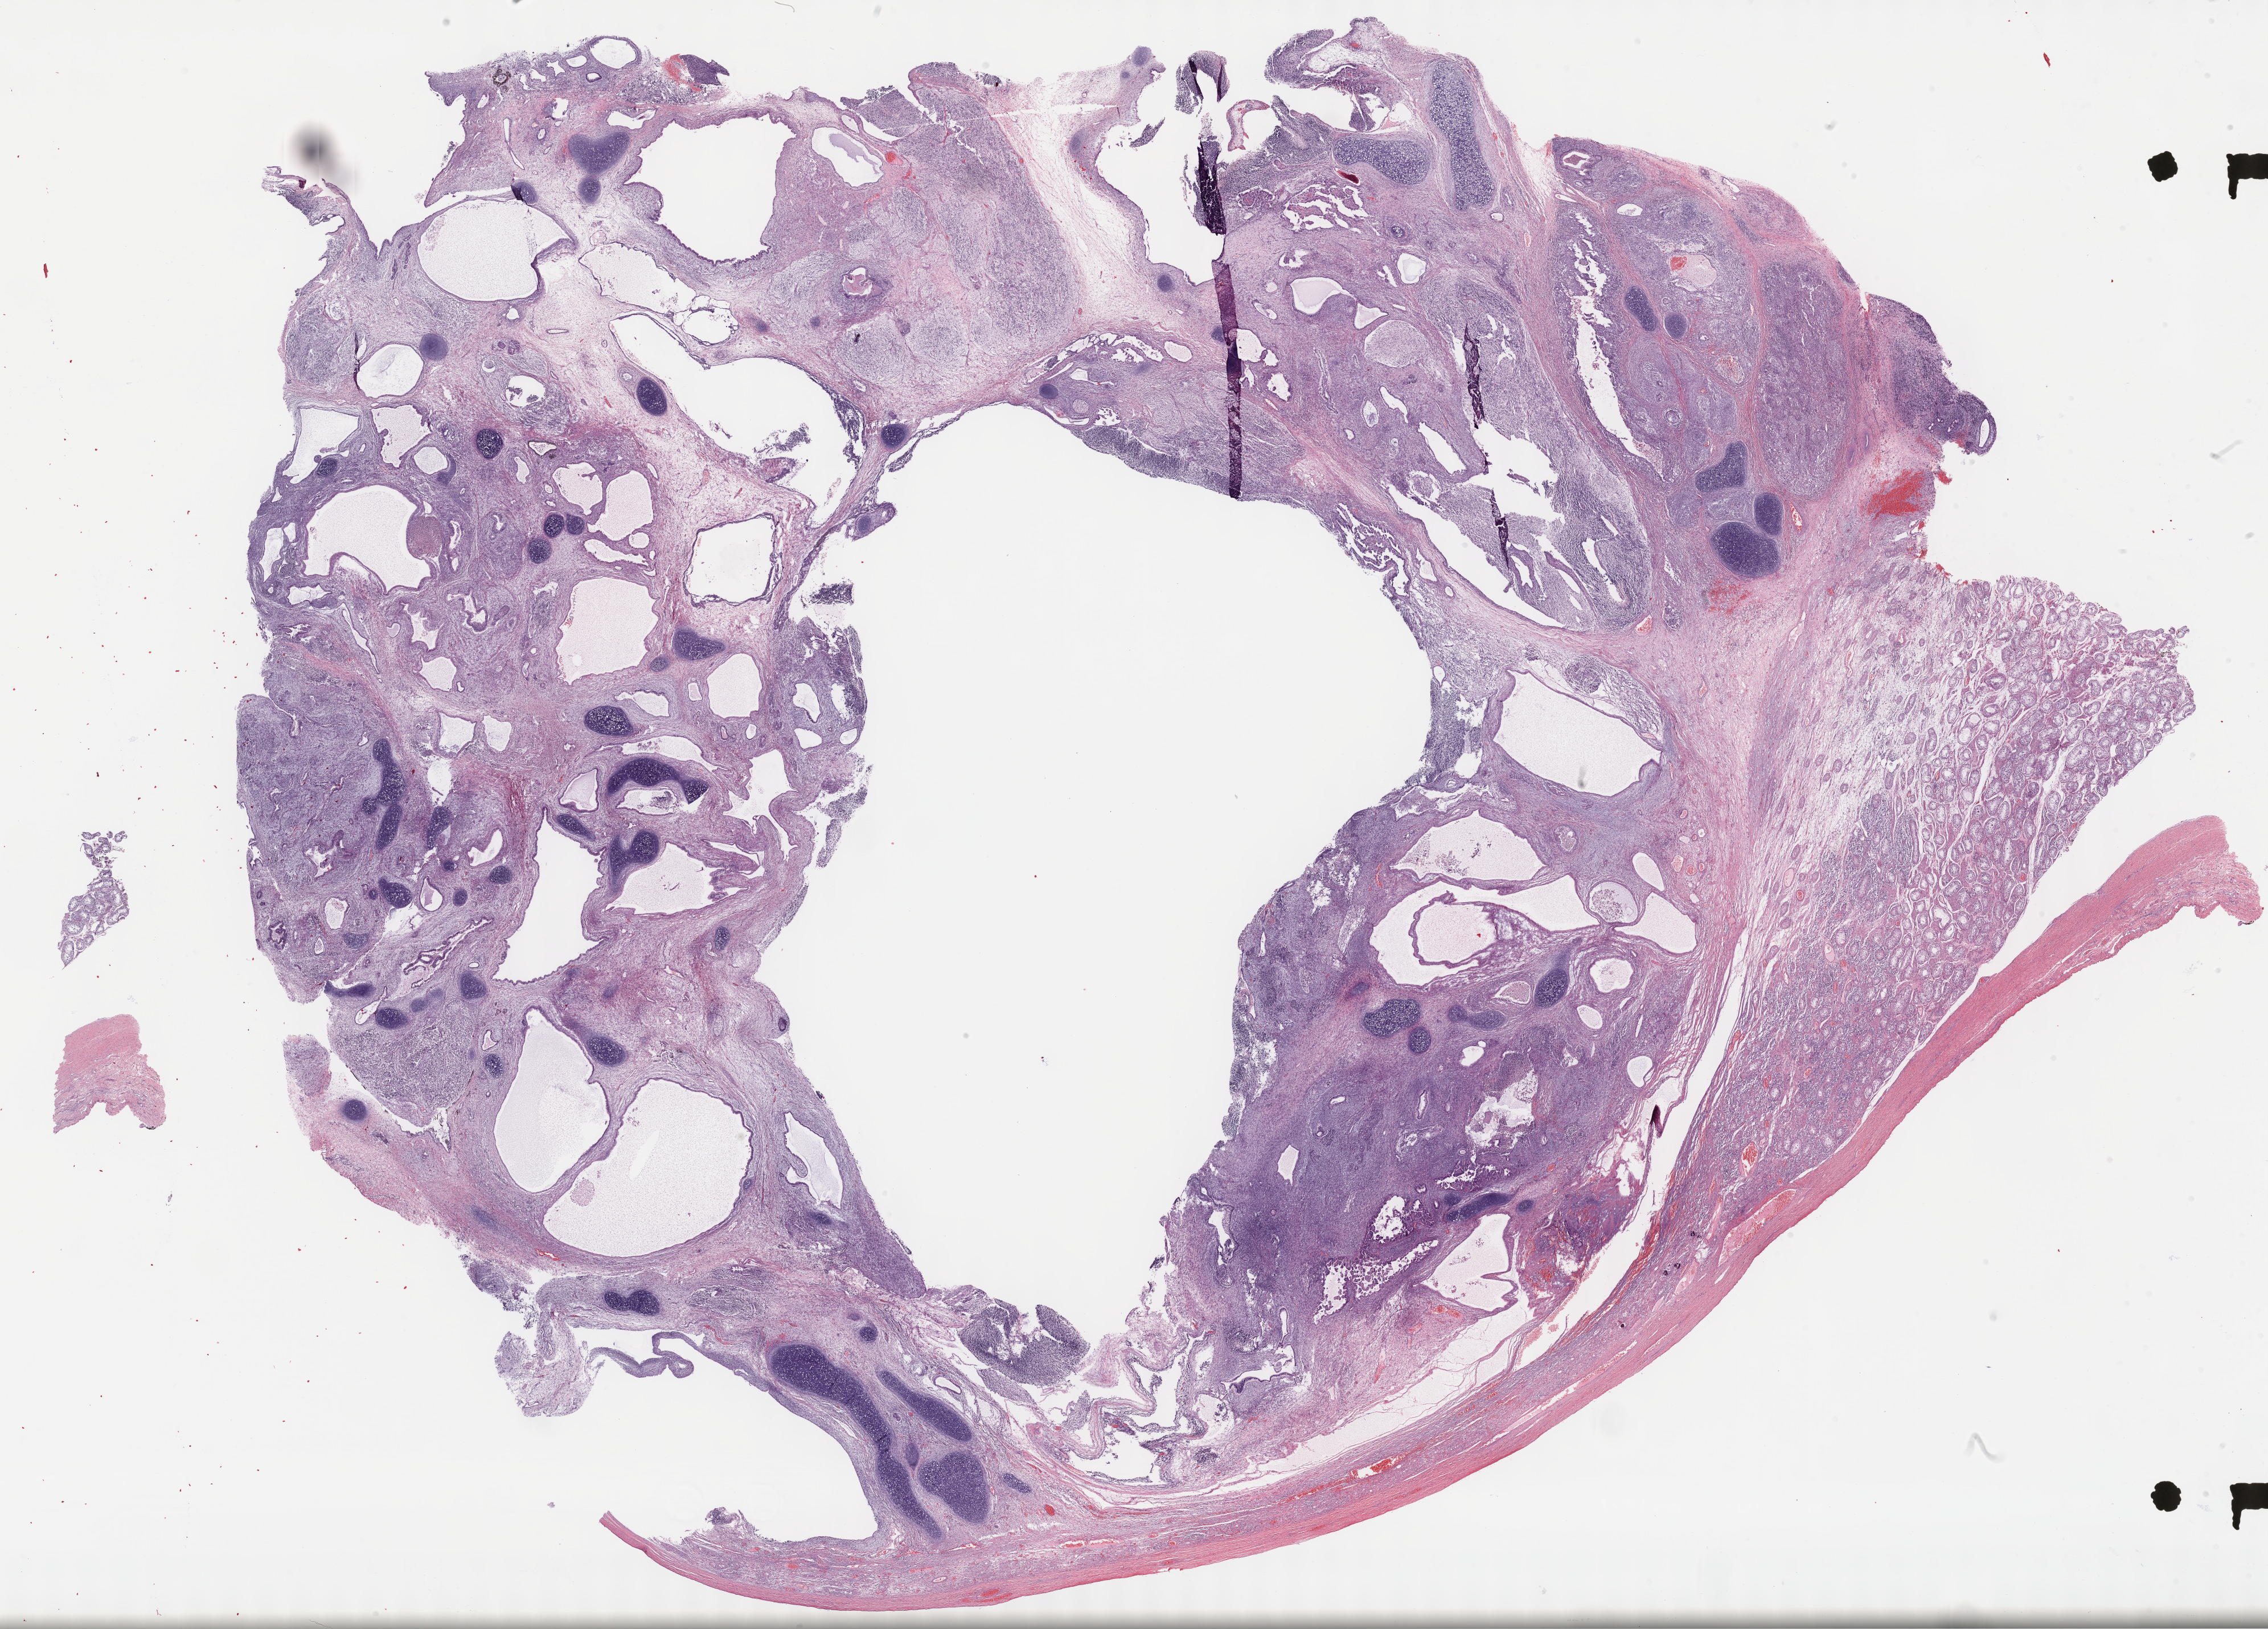
H&E-stained whole-slide image — whole scanned area (about 32.2 x 23.1 mm, acquisition: 40x scan) shown as a low-resolution overview, formalin-fixed paraffin-embedded (FFPE) diagnostic section, sample: primary tumour, testis. Patient: male, age at initial diagnosis 37 years.
Histologic diagnosis: Teratocarcinoma. AJCC pathologic stage: IS.